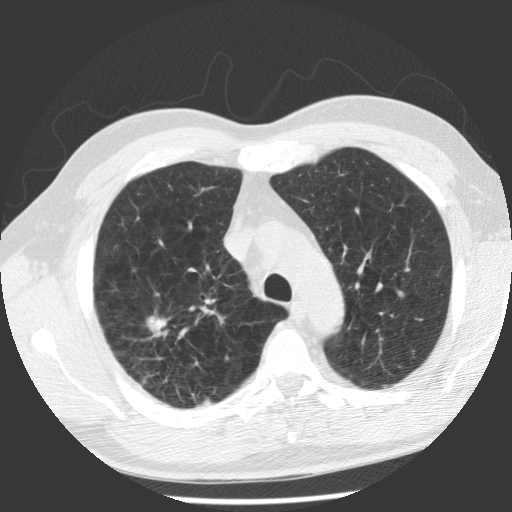
Axial slice from a low-dose chest CT screening exam, baseline screening round, lung window (W 1500 / L -600 HU), standard (soft-tissue) reconstruction kernel (STANDARD), 140 kVp, 512 × 512 image matrix, field of view 344 × 344 mm. Male participant, aged 62 years at enrolment.
Expert reader's lesion annotation, box from (x=116, y=301) to (x=194, y=379) px. The screening reader recorded 2 non-calcified nodules or masses ≥4 mm on this exam; which of them this box marks is not recorded. Later outcome: lung cancer diagnosed 71 days after this screen — adenocarcinoma, NOS, right upper lobe, poorly differentiated (G3), stage IV (AJCC 6th edition), 30 mm at pathology.